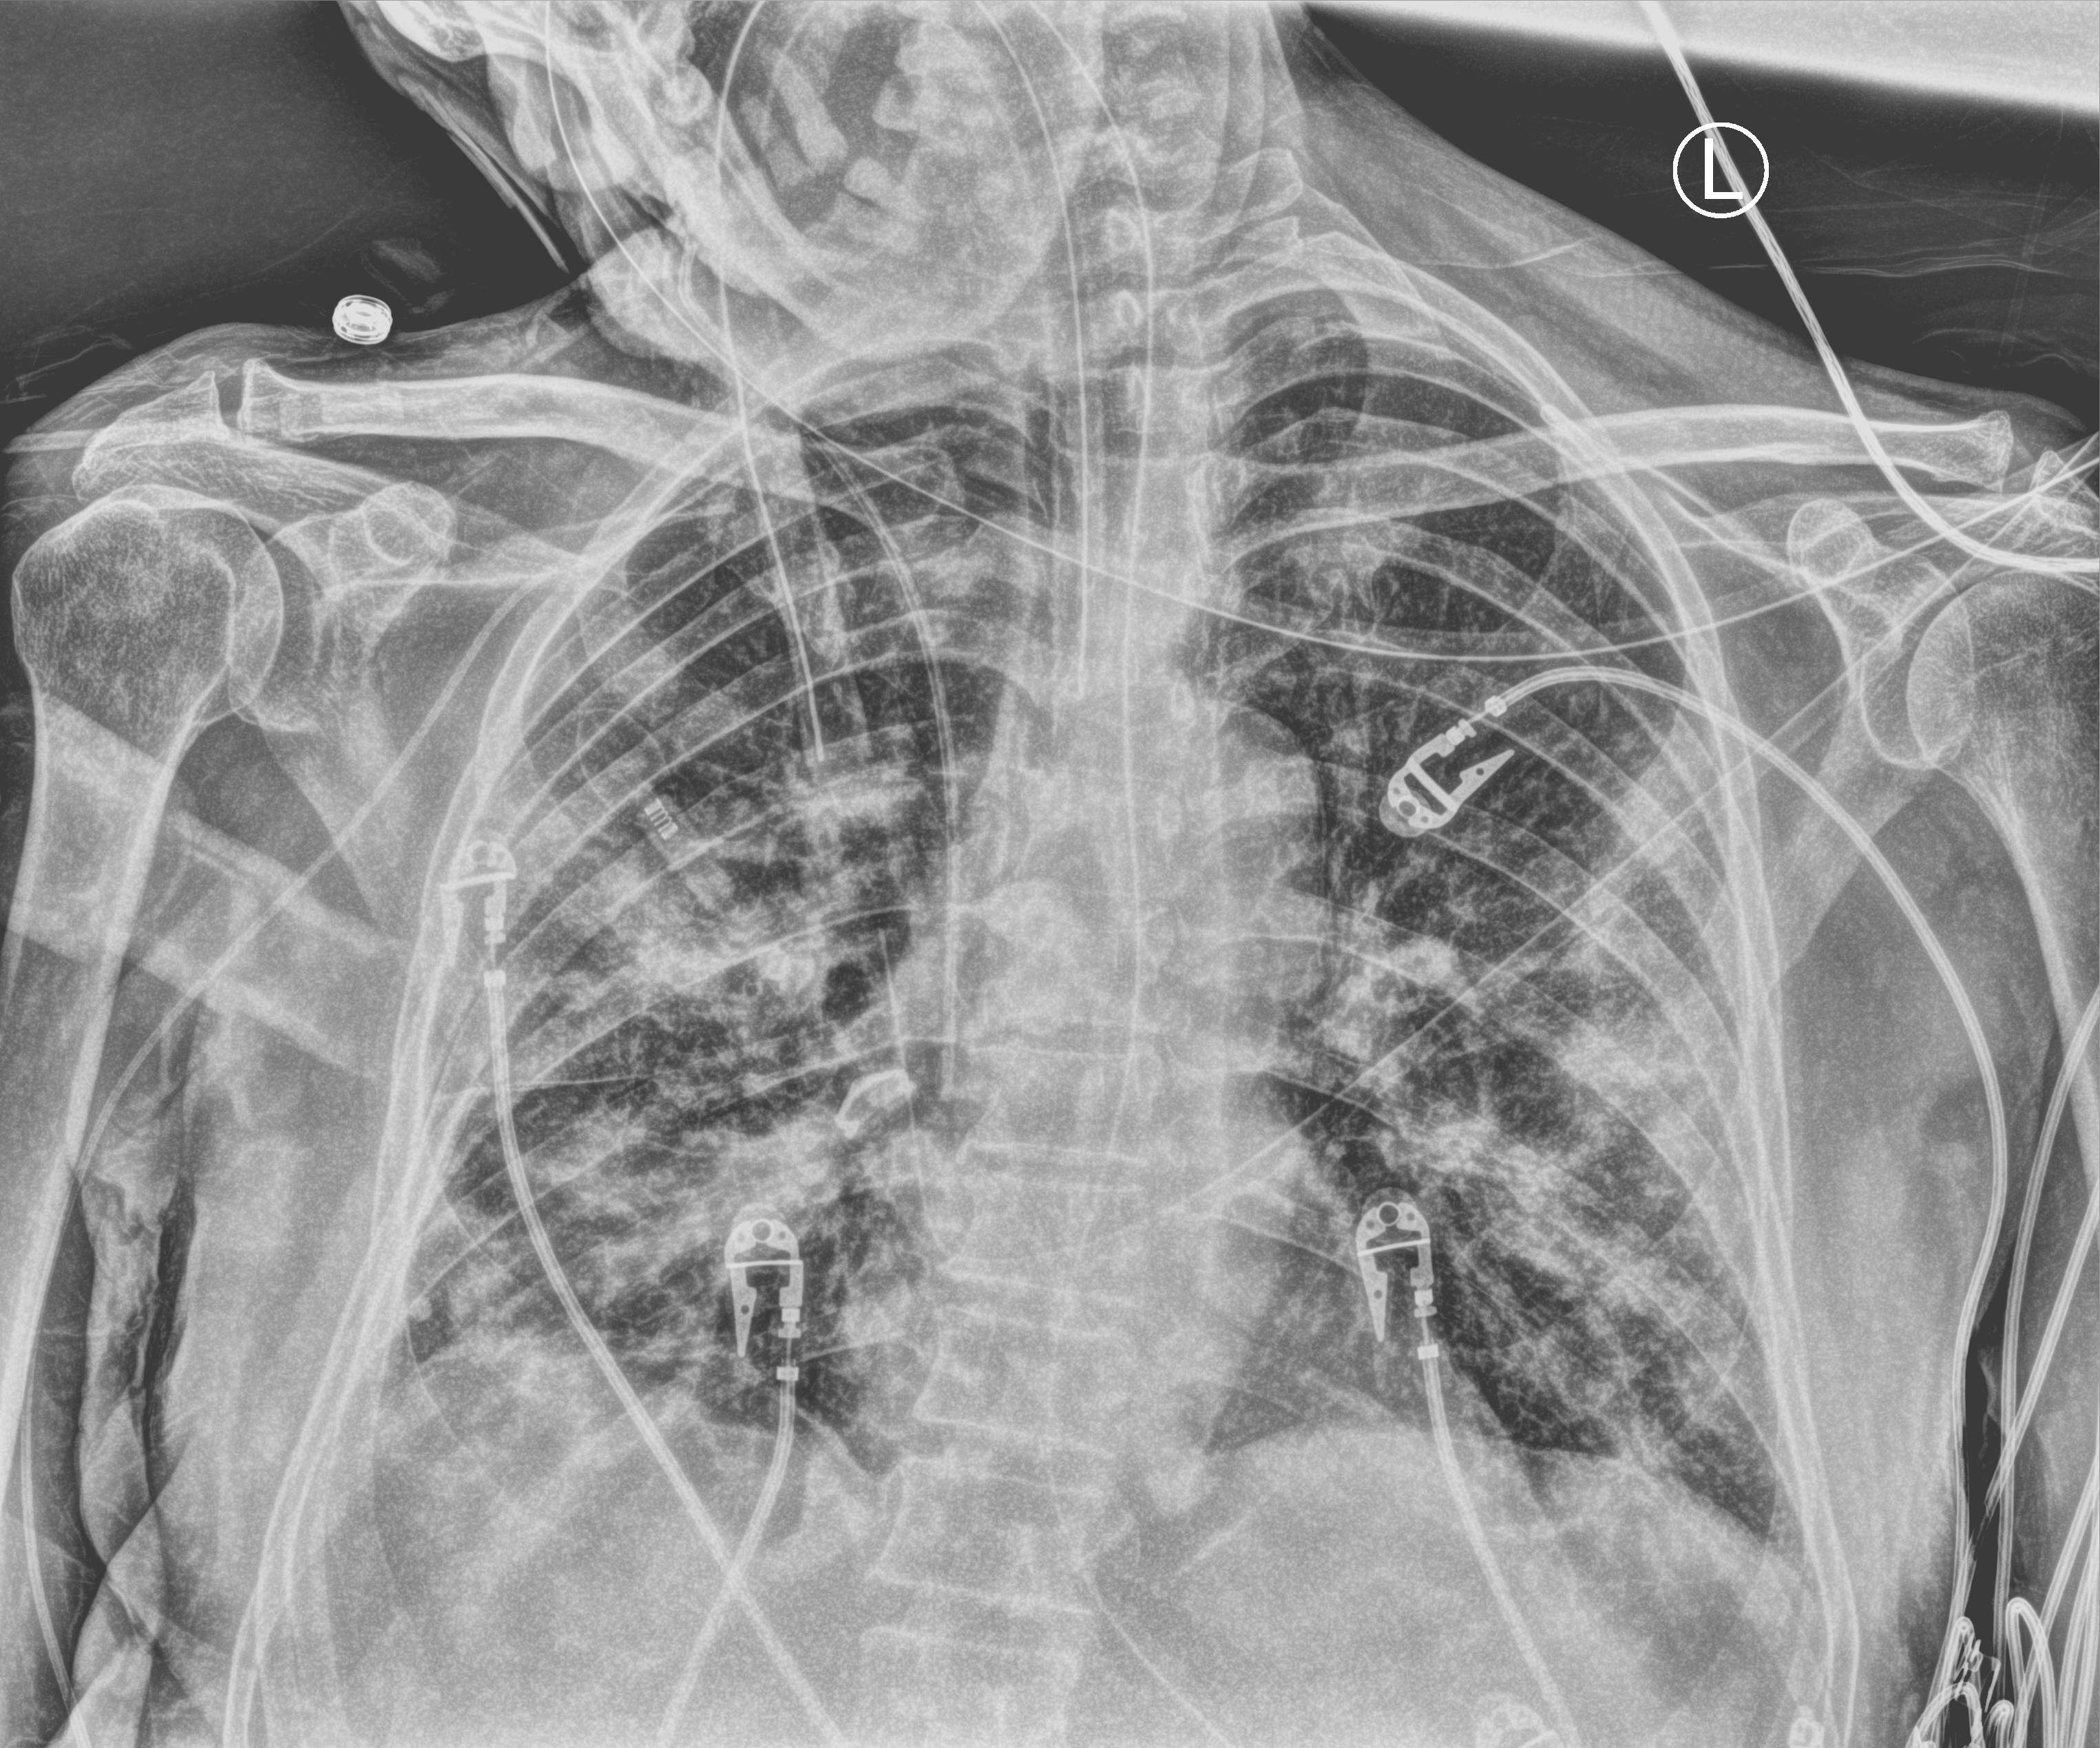
Bedside chest radiograph (computed radiography); anteroposterior (AP) projection. Male patient hospitalised with COVID-19, age 75–90 years.
Hospital-stay facts (about this admission, not read from this image; timing relative to this image not recorded): mechanically ventilated during this hospital stay: yes; admitted to intensive care during this hospital stay: yes.